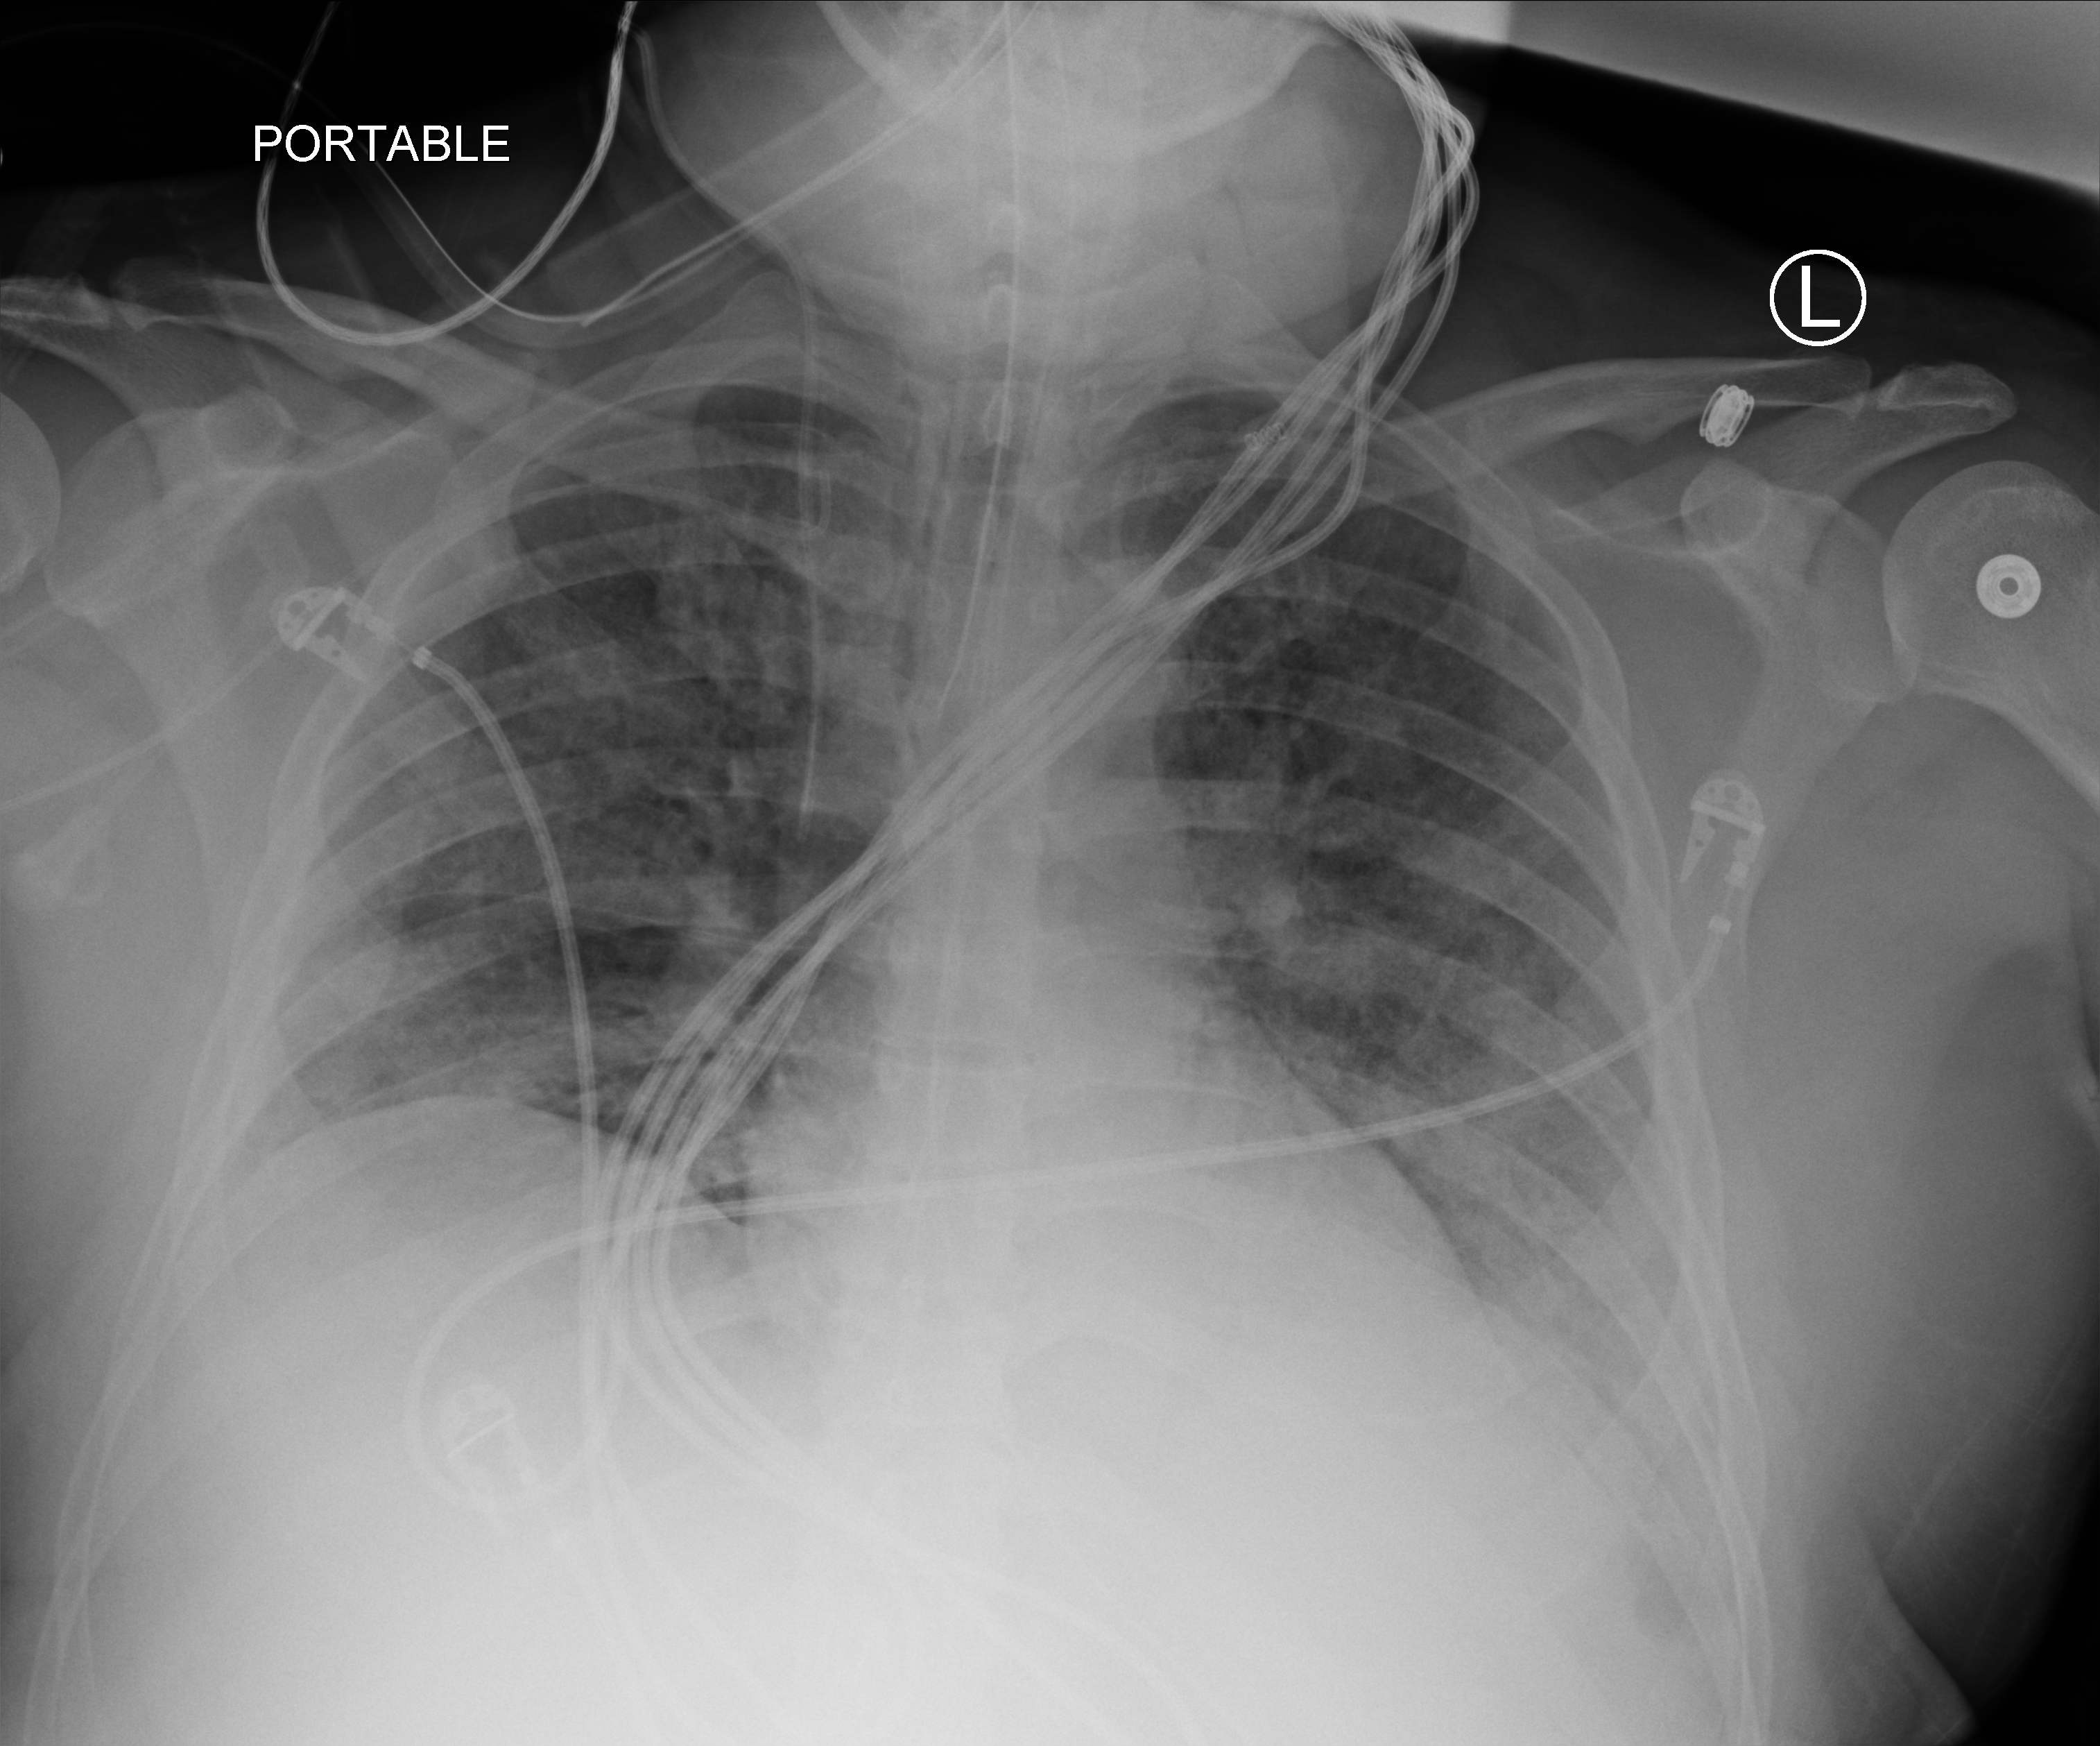
Chest X-ray (portable), anteroposterior (AP) projection. Male patient hospitalised with COVID-19, age 18–59 years.
Admission-level facts for this patient (not findings on this image; timing relative to this image not recorded): diabetes (admission record): no; mechanically ventilated during this hospital stay: yes.